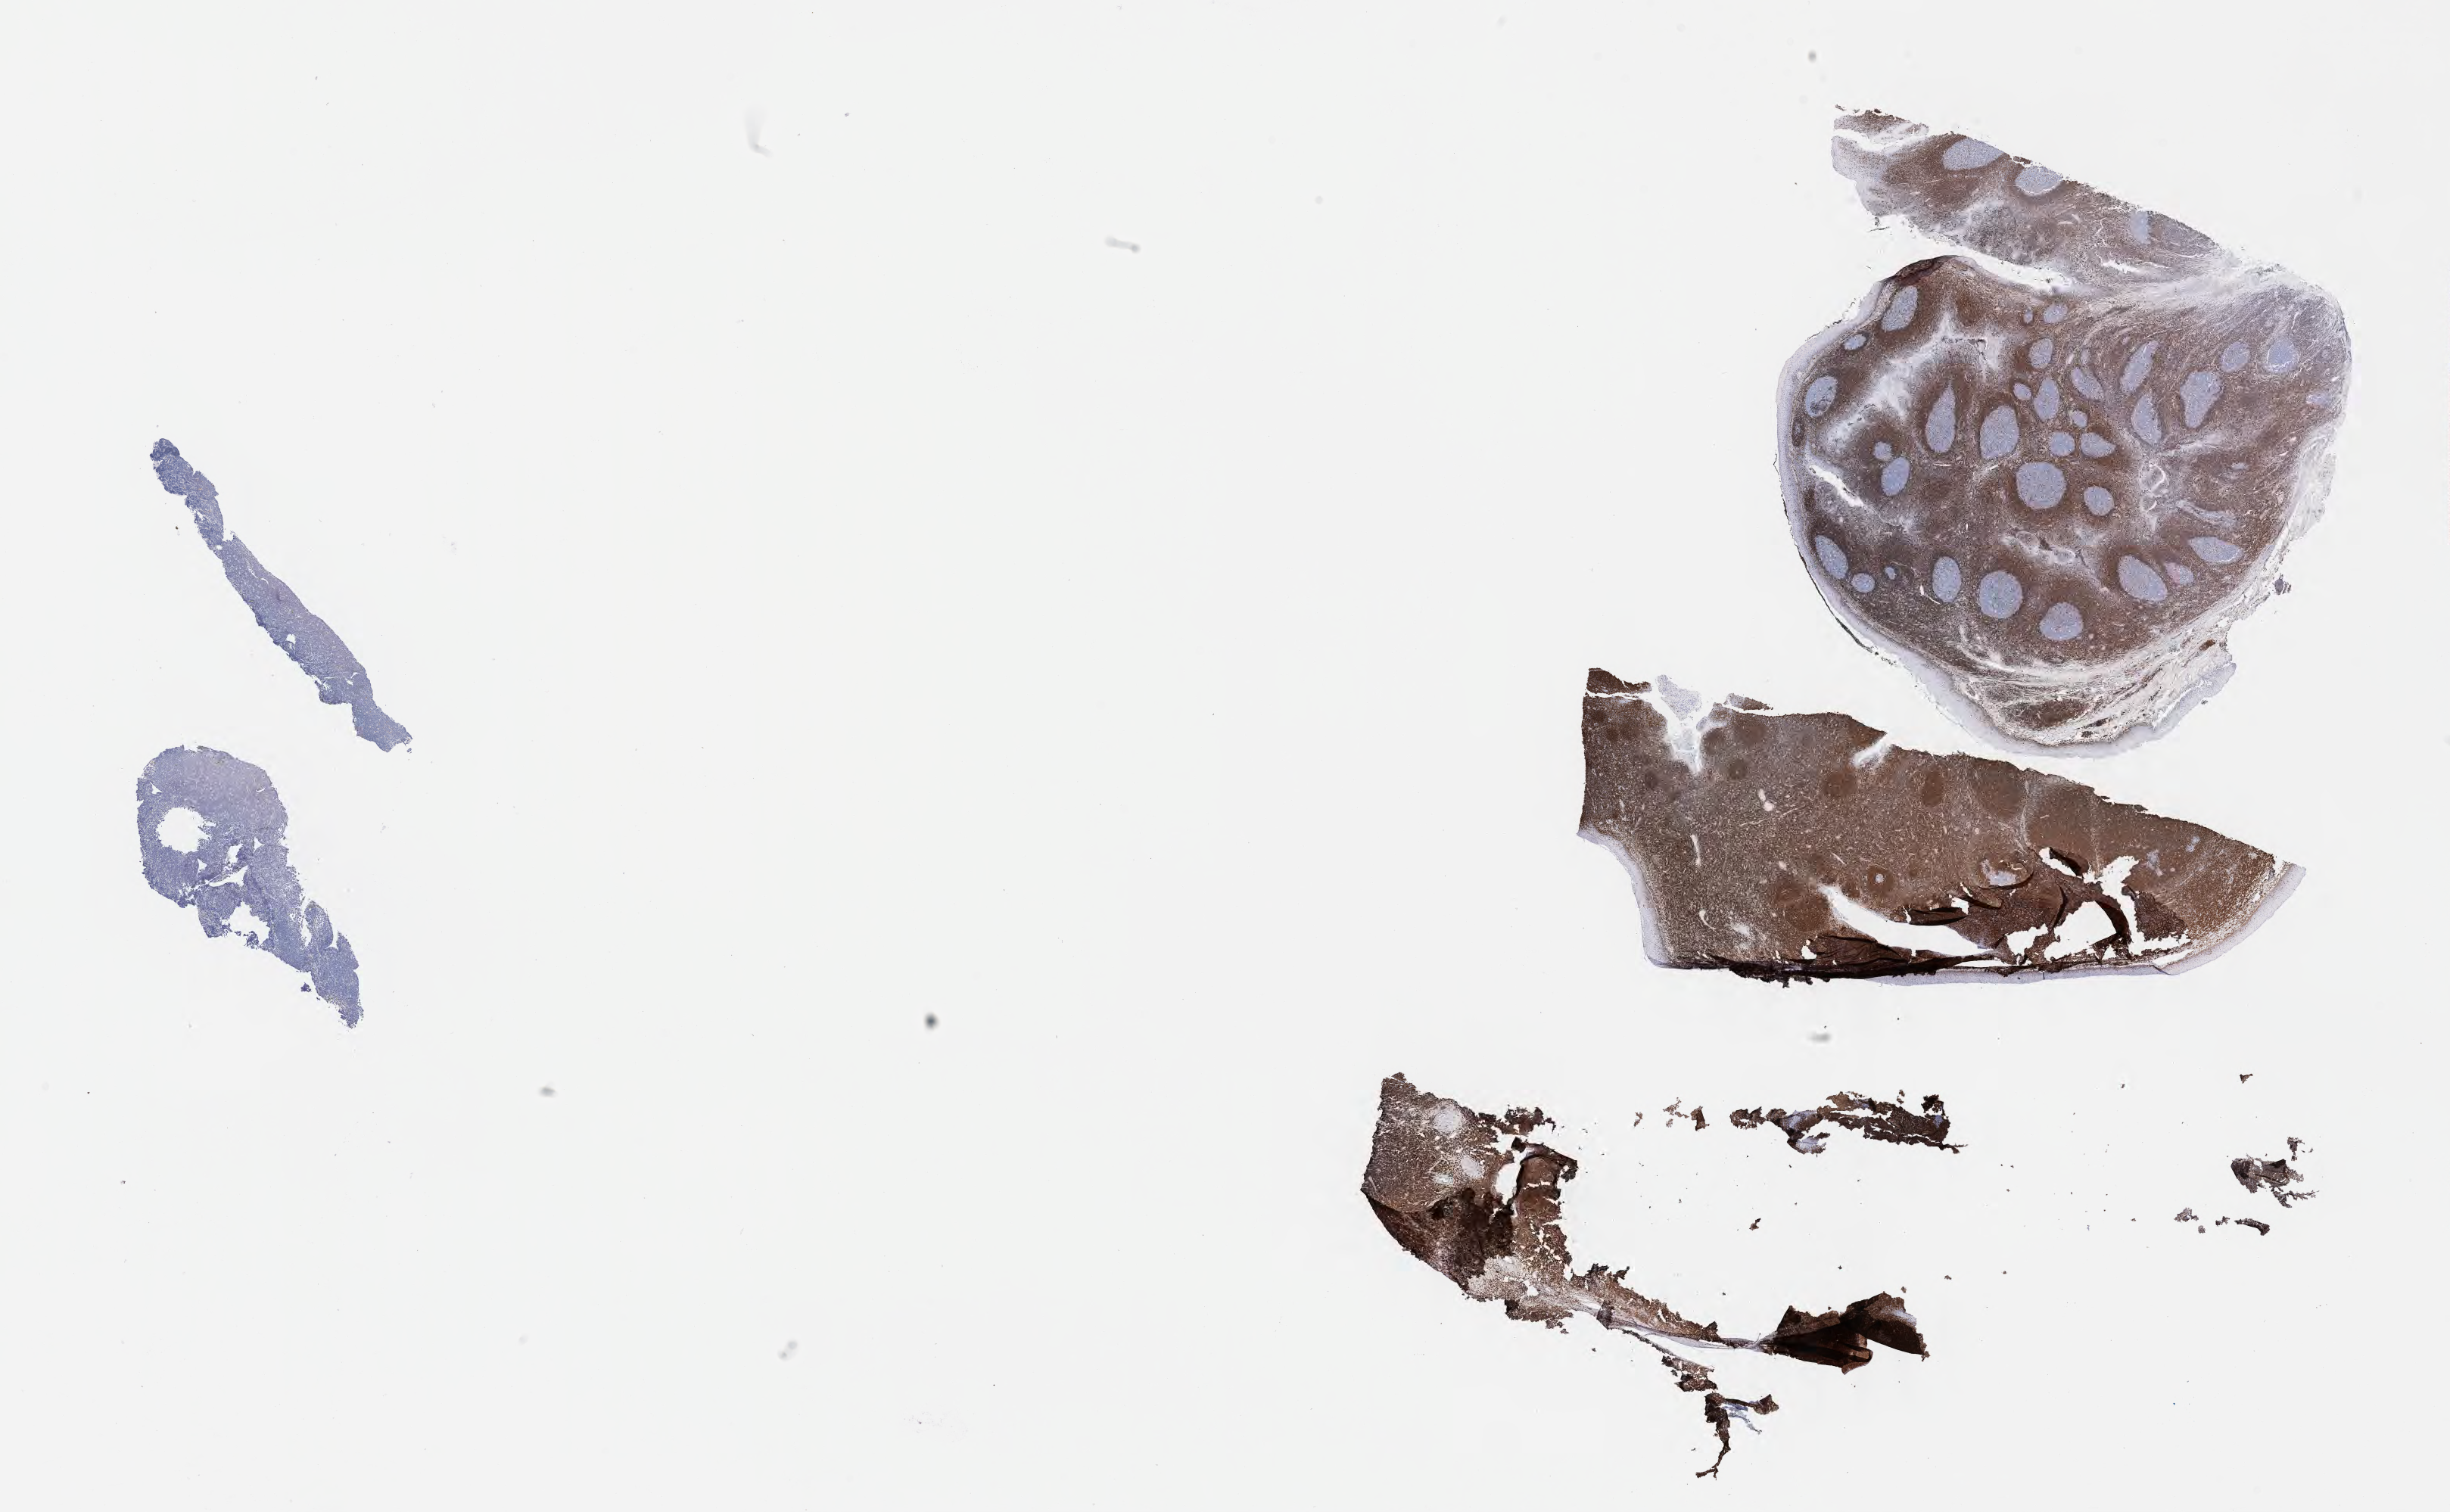
Whole-slide image, immunohistochemical stain for BCL2 — whole scanned area (about 26.2 x 16.1 mm) shown as a low-resolution overview, specimen: tumor tissue. Patient: male, age at initial diagnosis 8 years.
Diagnosis: Burkitt lymphoma, NOS.